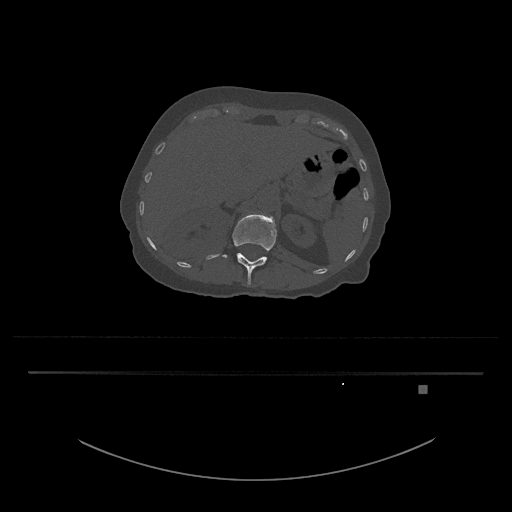
CT including the spine, one axial slice; position 548 of 797 along the scan axis; reconstruction kernel Br40s/3; bone window (W 1800 / L 400 HU); 512 × 512 image matrix, field of view 500 × 500 mm. Patient: female, 57 years. From the clinical record (not read from this slice): primary cancer: cervical.
Annotated regions visible in this slice (semi-automatically segmented with operator editing):
- L1 vertebra: bounding box <206,214,277,285> (left, top, right, bottom; pixels)